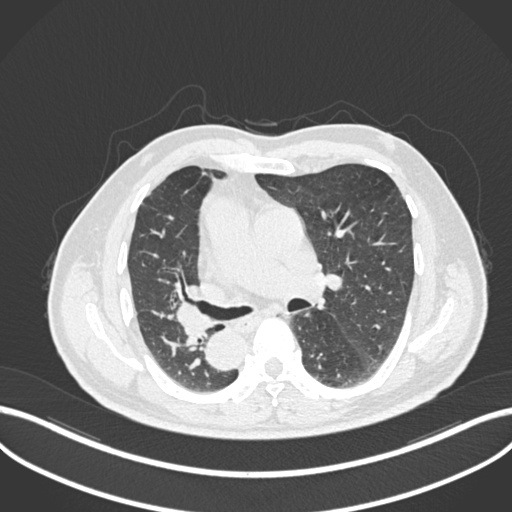
Chest CT, one axial slice. Slice 127 of 206 in the series (ordered by position). Reconstruction kernel B30f. 120 kVp. Lung window (W 1500 / L -600 HU). 1 mm slice thickness. 512 × 512 image matrix, field of view 400 × 400 mm. Male patient, age 67 years. From the clinical record (not read from this slice): clinical TNM (as recorded): T2a N0 M0.
Annotated regions visible in this slice (bounding box drawn by a radiologist):
- lung tumour (recorded histology: squamous cell carcinoma): bounding box <170,300,215,348> (left, top, right, bottom; pixels)